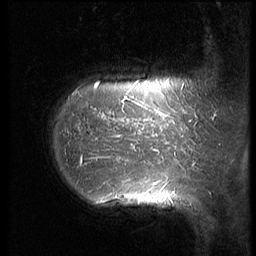
Breast MRI (dynamic contrast-enhanced), one sagittal slice; slice 11 of 64 in the series (ordered by position); 3 images stored at this slice position (order not interpretable as contrast timing); 1.5 T; TE 4.2 ms, TR 9 ms; 2.5 mm slice thickness; 256 × 256 image matrix. Patient: female, 39 years. From the clinical record (not read from this slice): setting: breast cancer imaged before/during neoadjuvant chemotherapy; receptor status: HER2-positive.
Structures marked on this image (semi-automatically segmented with operator editing):
- analysis volume of interest (the breast-tissue region the enhancement analysis was run in; not a lesion): box from (x=47, y=47) to (x=210, y=239) px
- tumour enhancement mask (voxels above the 140 % enhancement threshold inside the analysis volume of interest): (x=76, y=81)–(x=192, y=185)